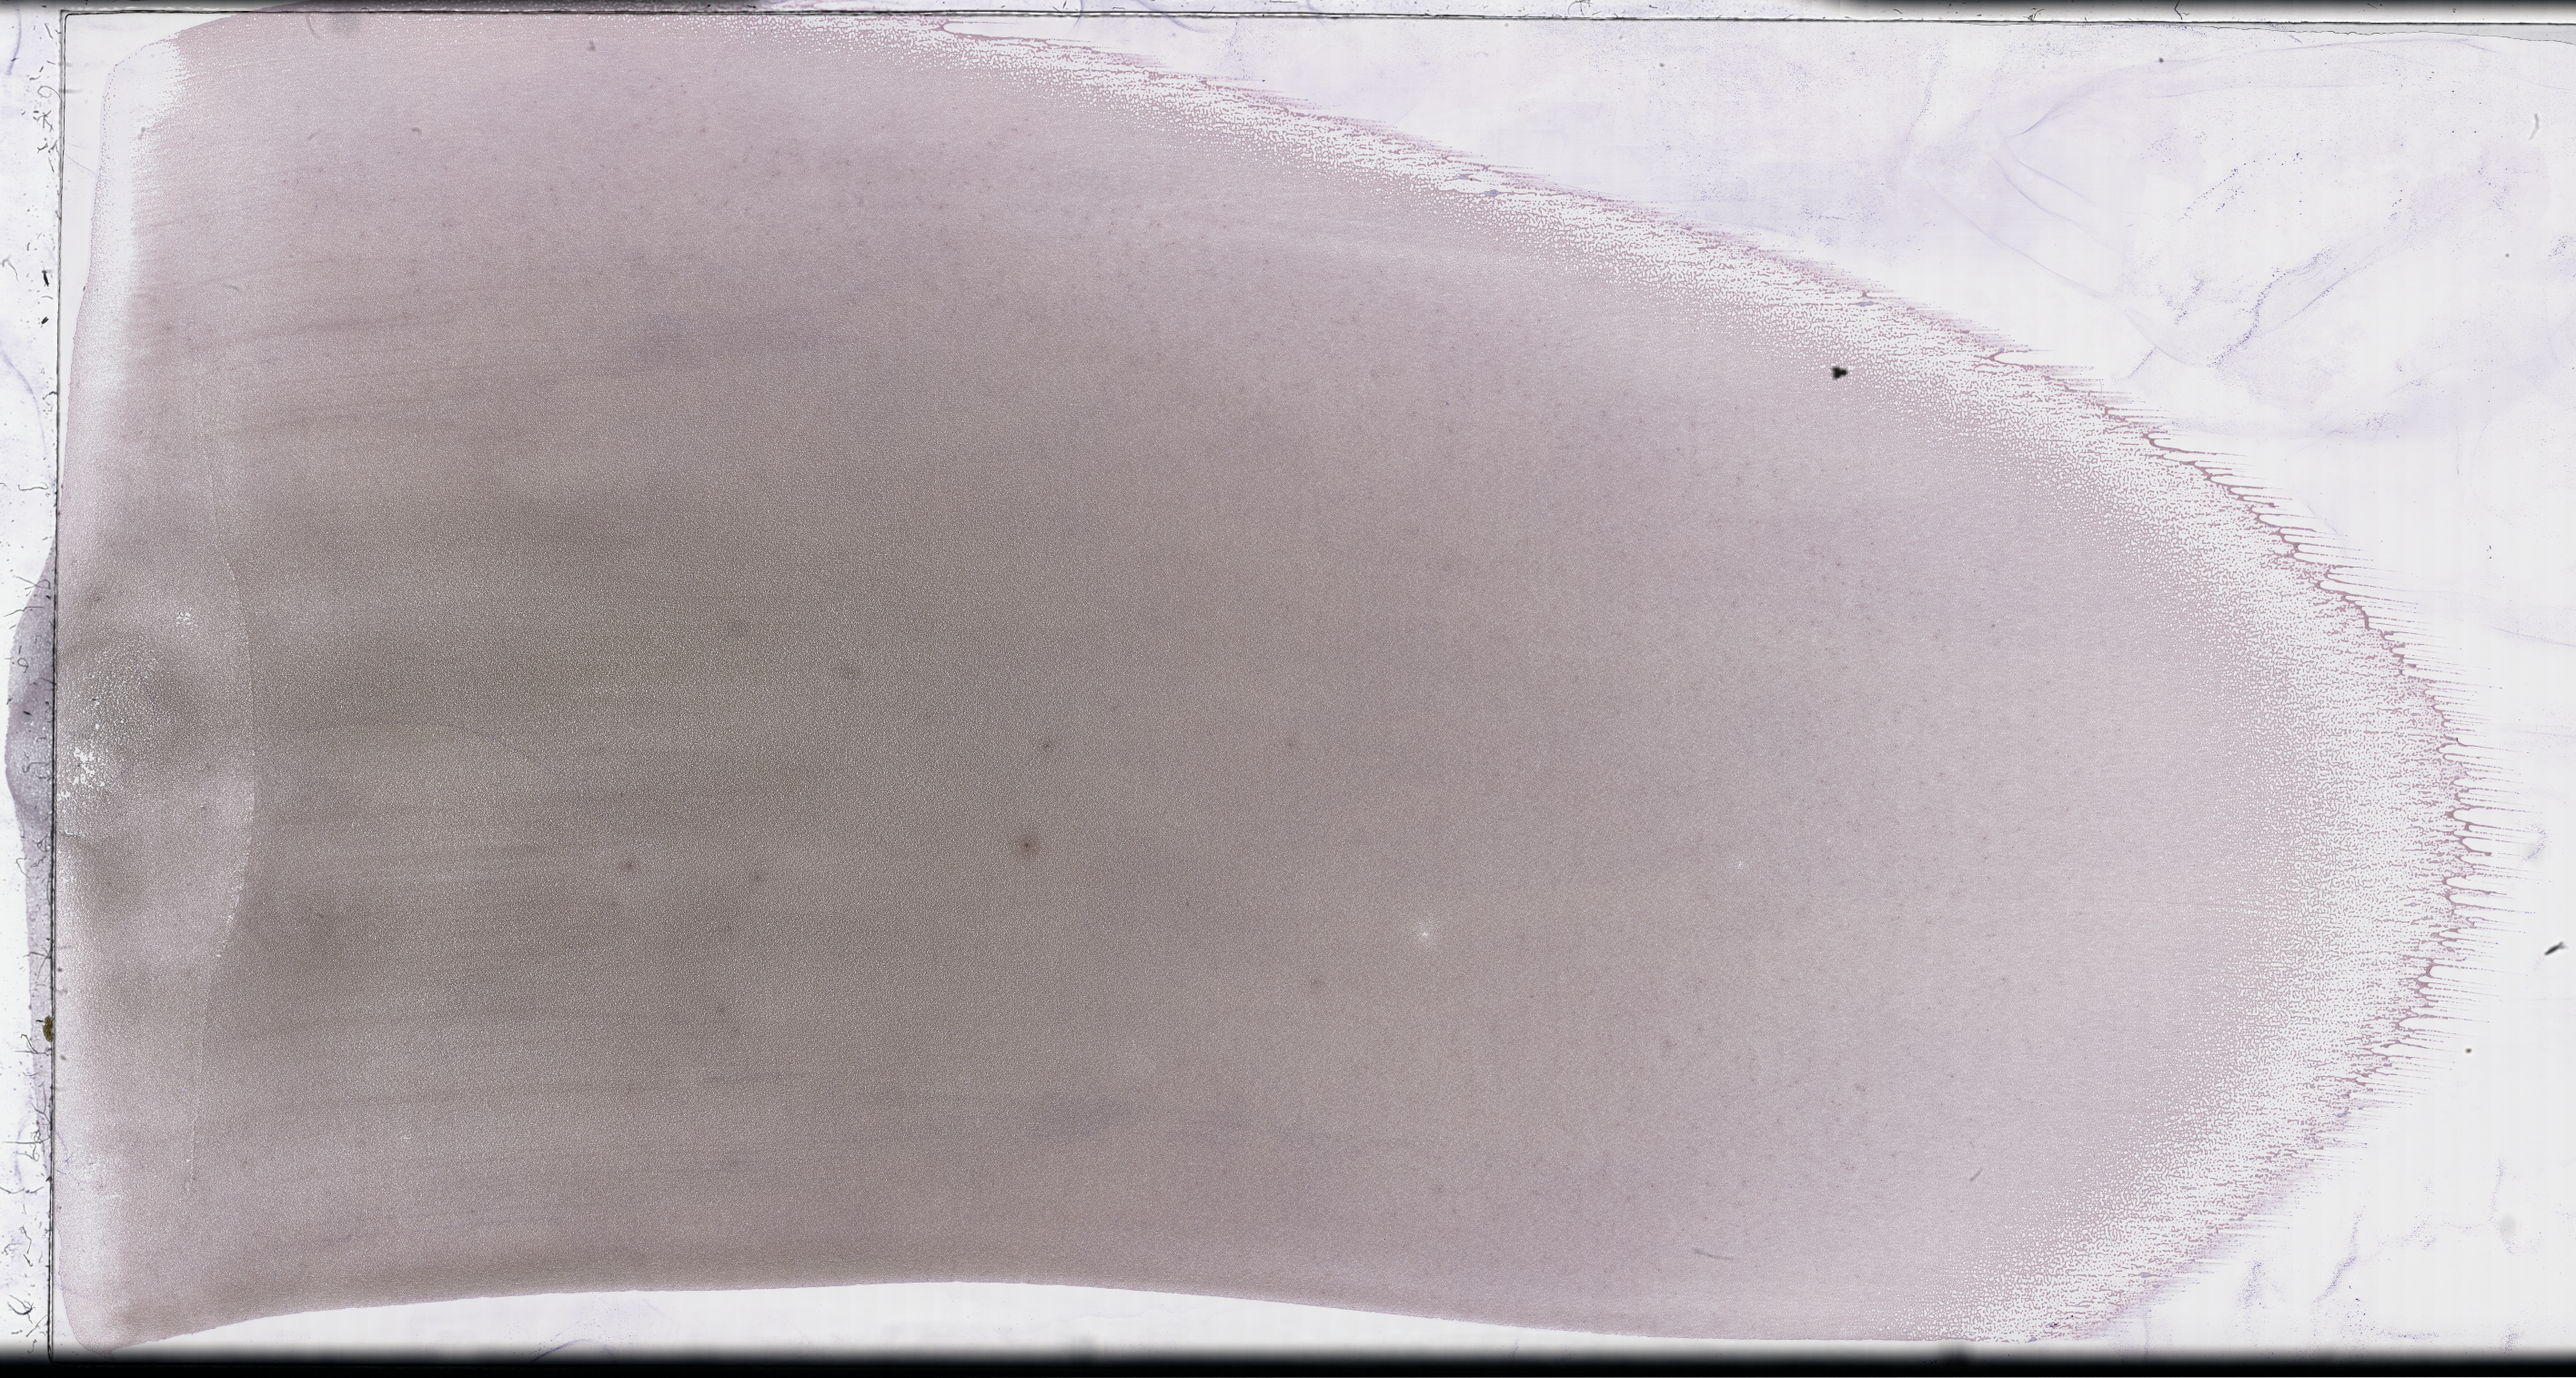
Wright-Giemsa-stained whole blood smear, whole-slide image — whole scanned area (about 45.7 x 24.5 mm) shown as a low-resolution overview, EDTA-anticoagulated smear, specimen time point: collected on treatment. Patient sex: male.
Patient diagnosis: Plasma Cell Myeloma.